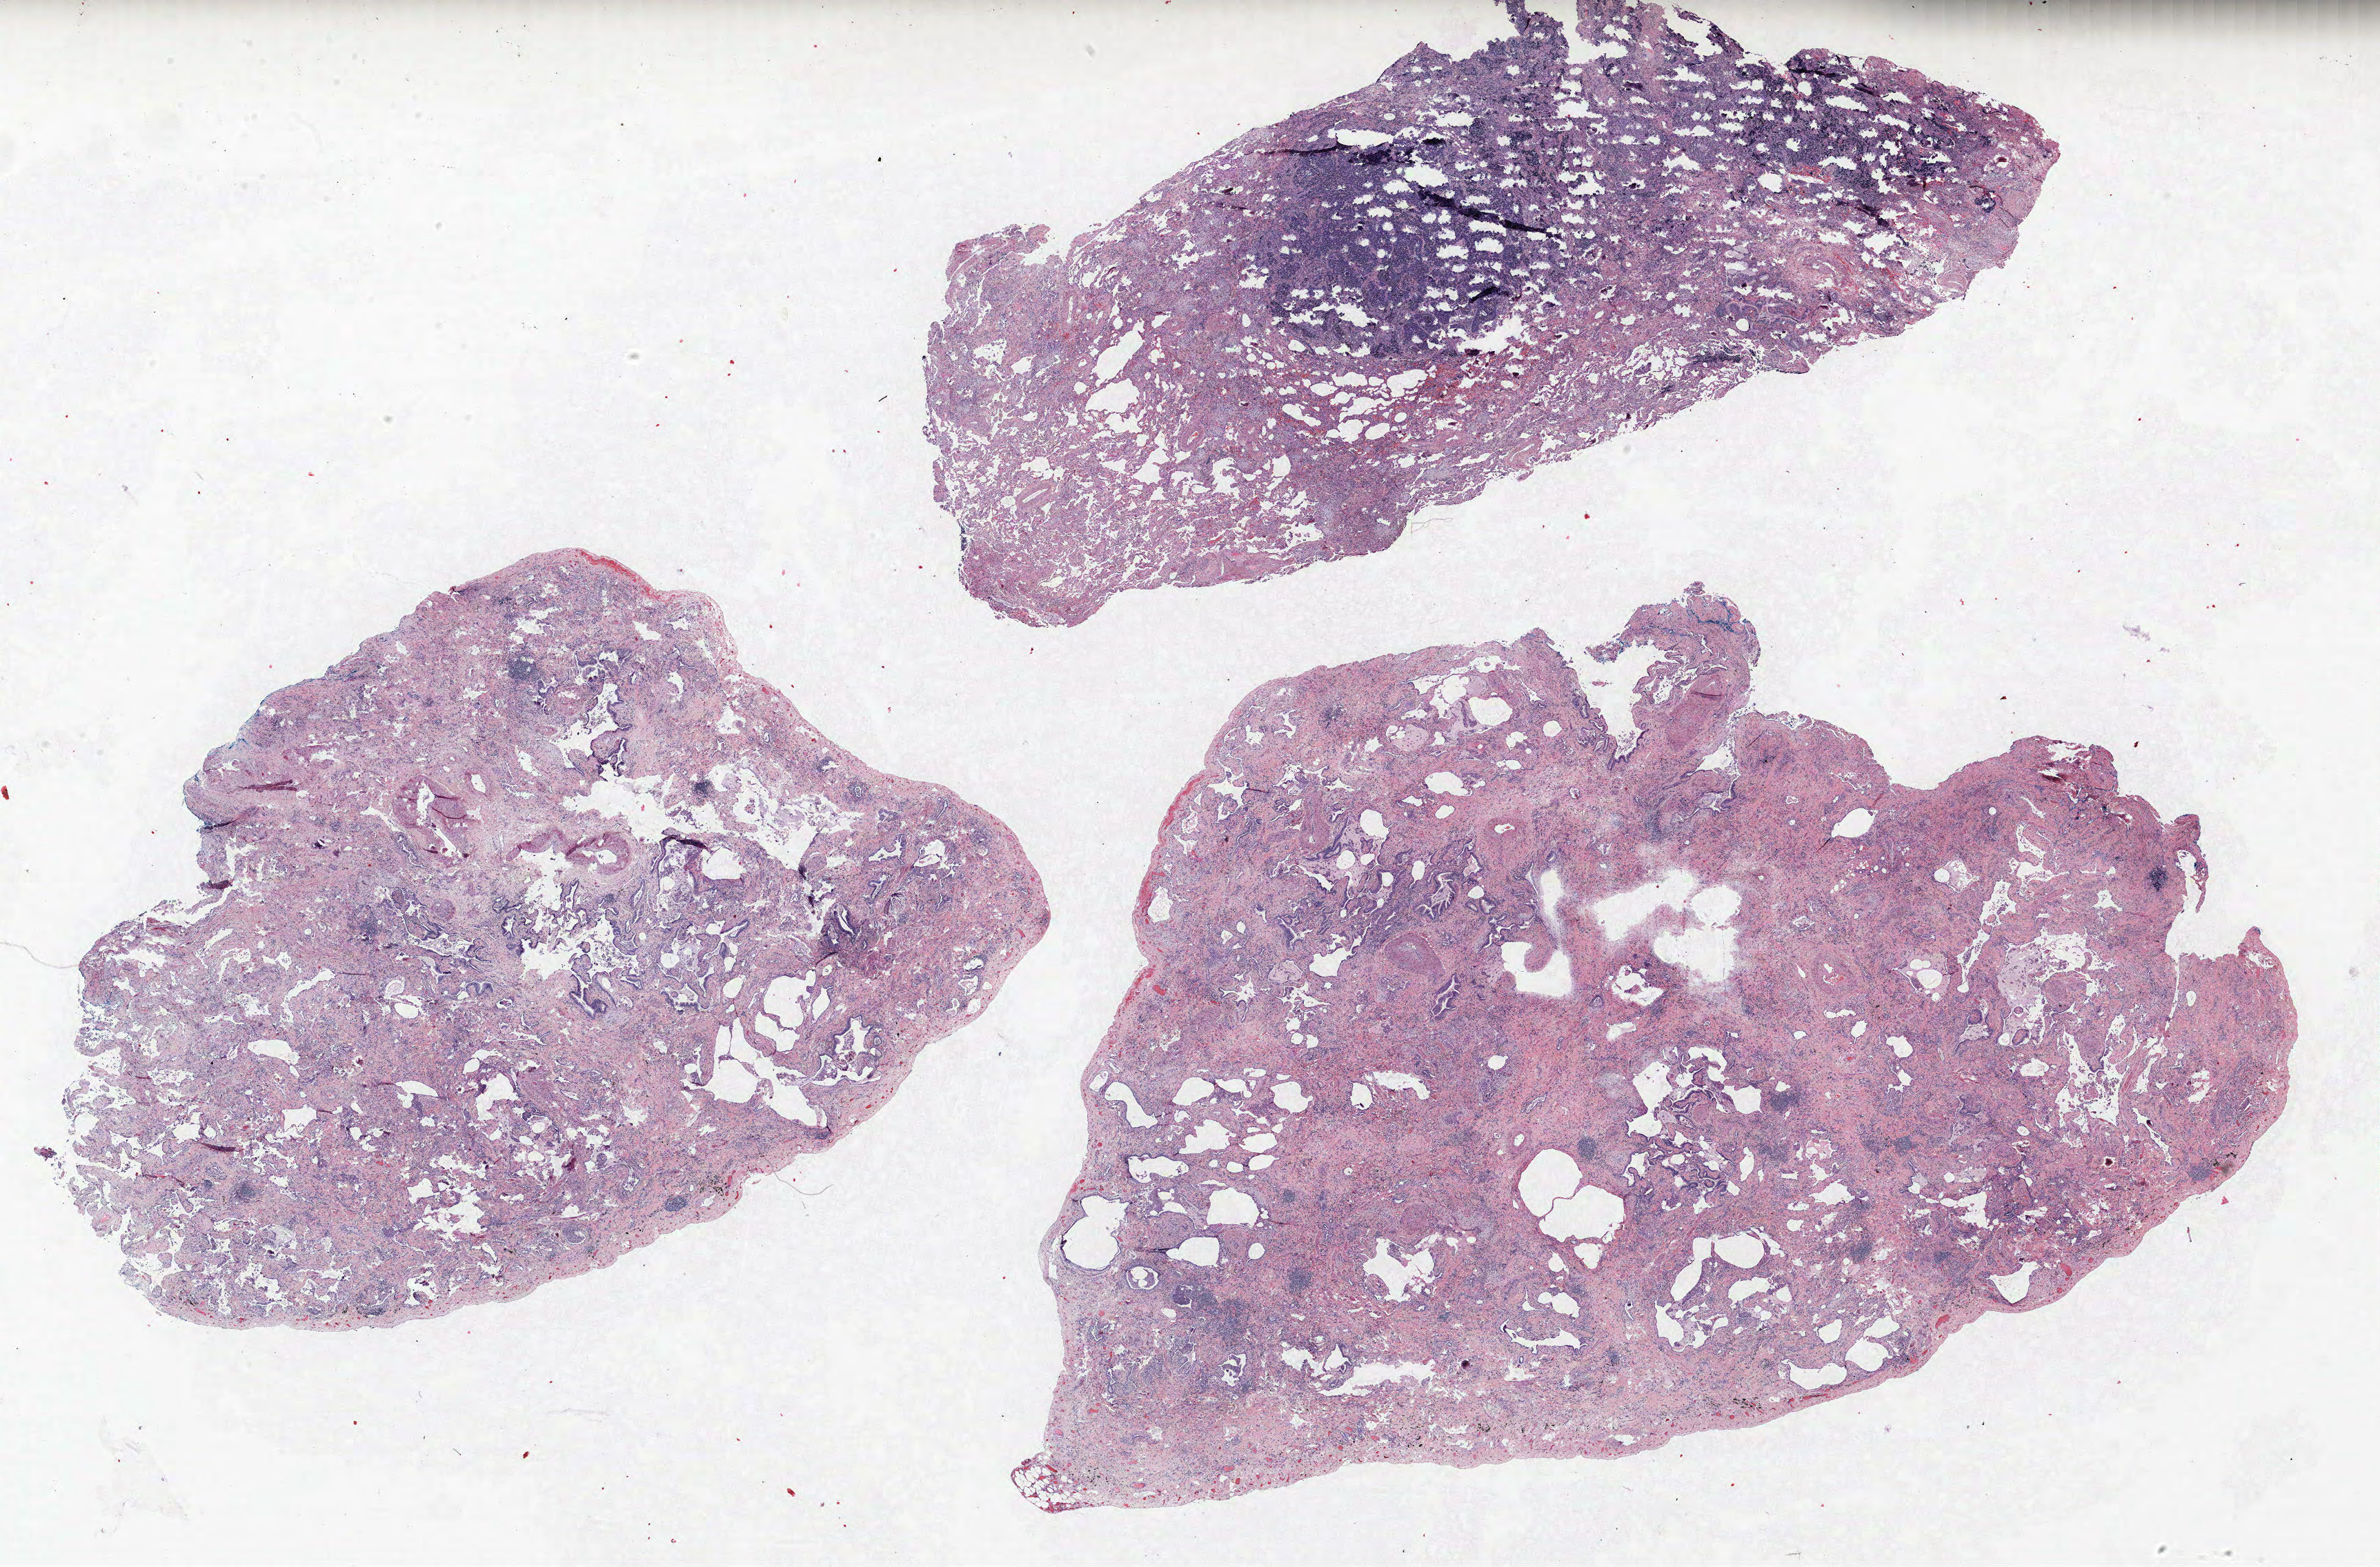
Whole-slide histology image, Hematoxylin and eosin (H&E) stained — shown as a low-resolution overview of the whole scanned area (about 27.6 x 18.2 mm, acquisition: 40x scan), FFPE section, lung tissue. Male, age 56 at enrolment.
Stage (AJCC 6th edition): IIIA. Participant's lung-cancer diagnosis: Large cell neuroendocrine carcinoma (ICD-O-3 8013/3). Primary tumour location (clinical record): right upper lobe. ICD-O-3 topography: upper lobe of lung (C34.1). Tumour size (pathology): 10 mm.